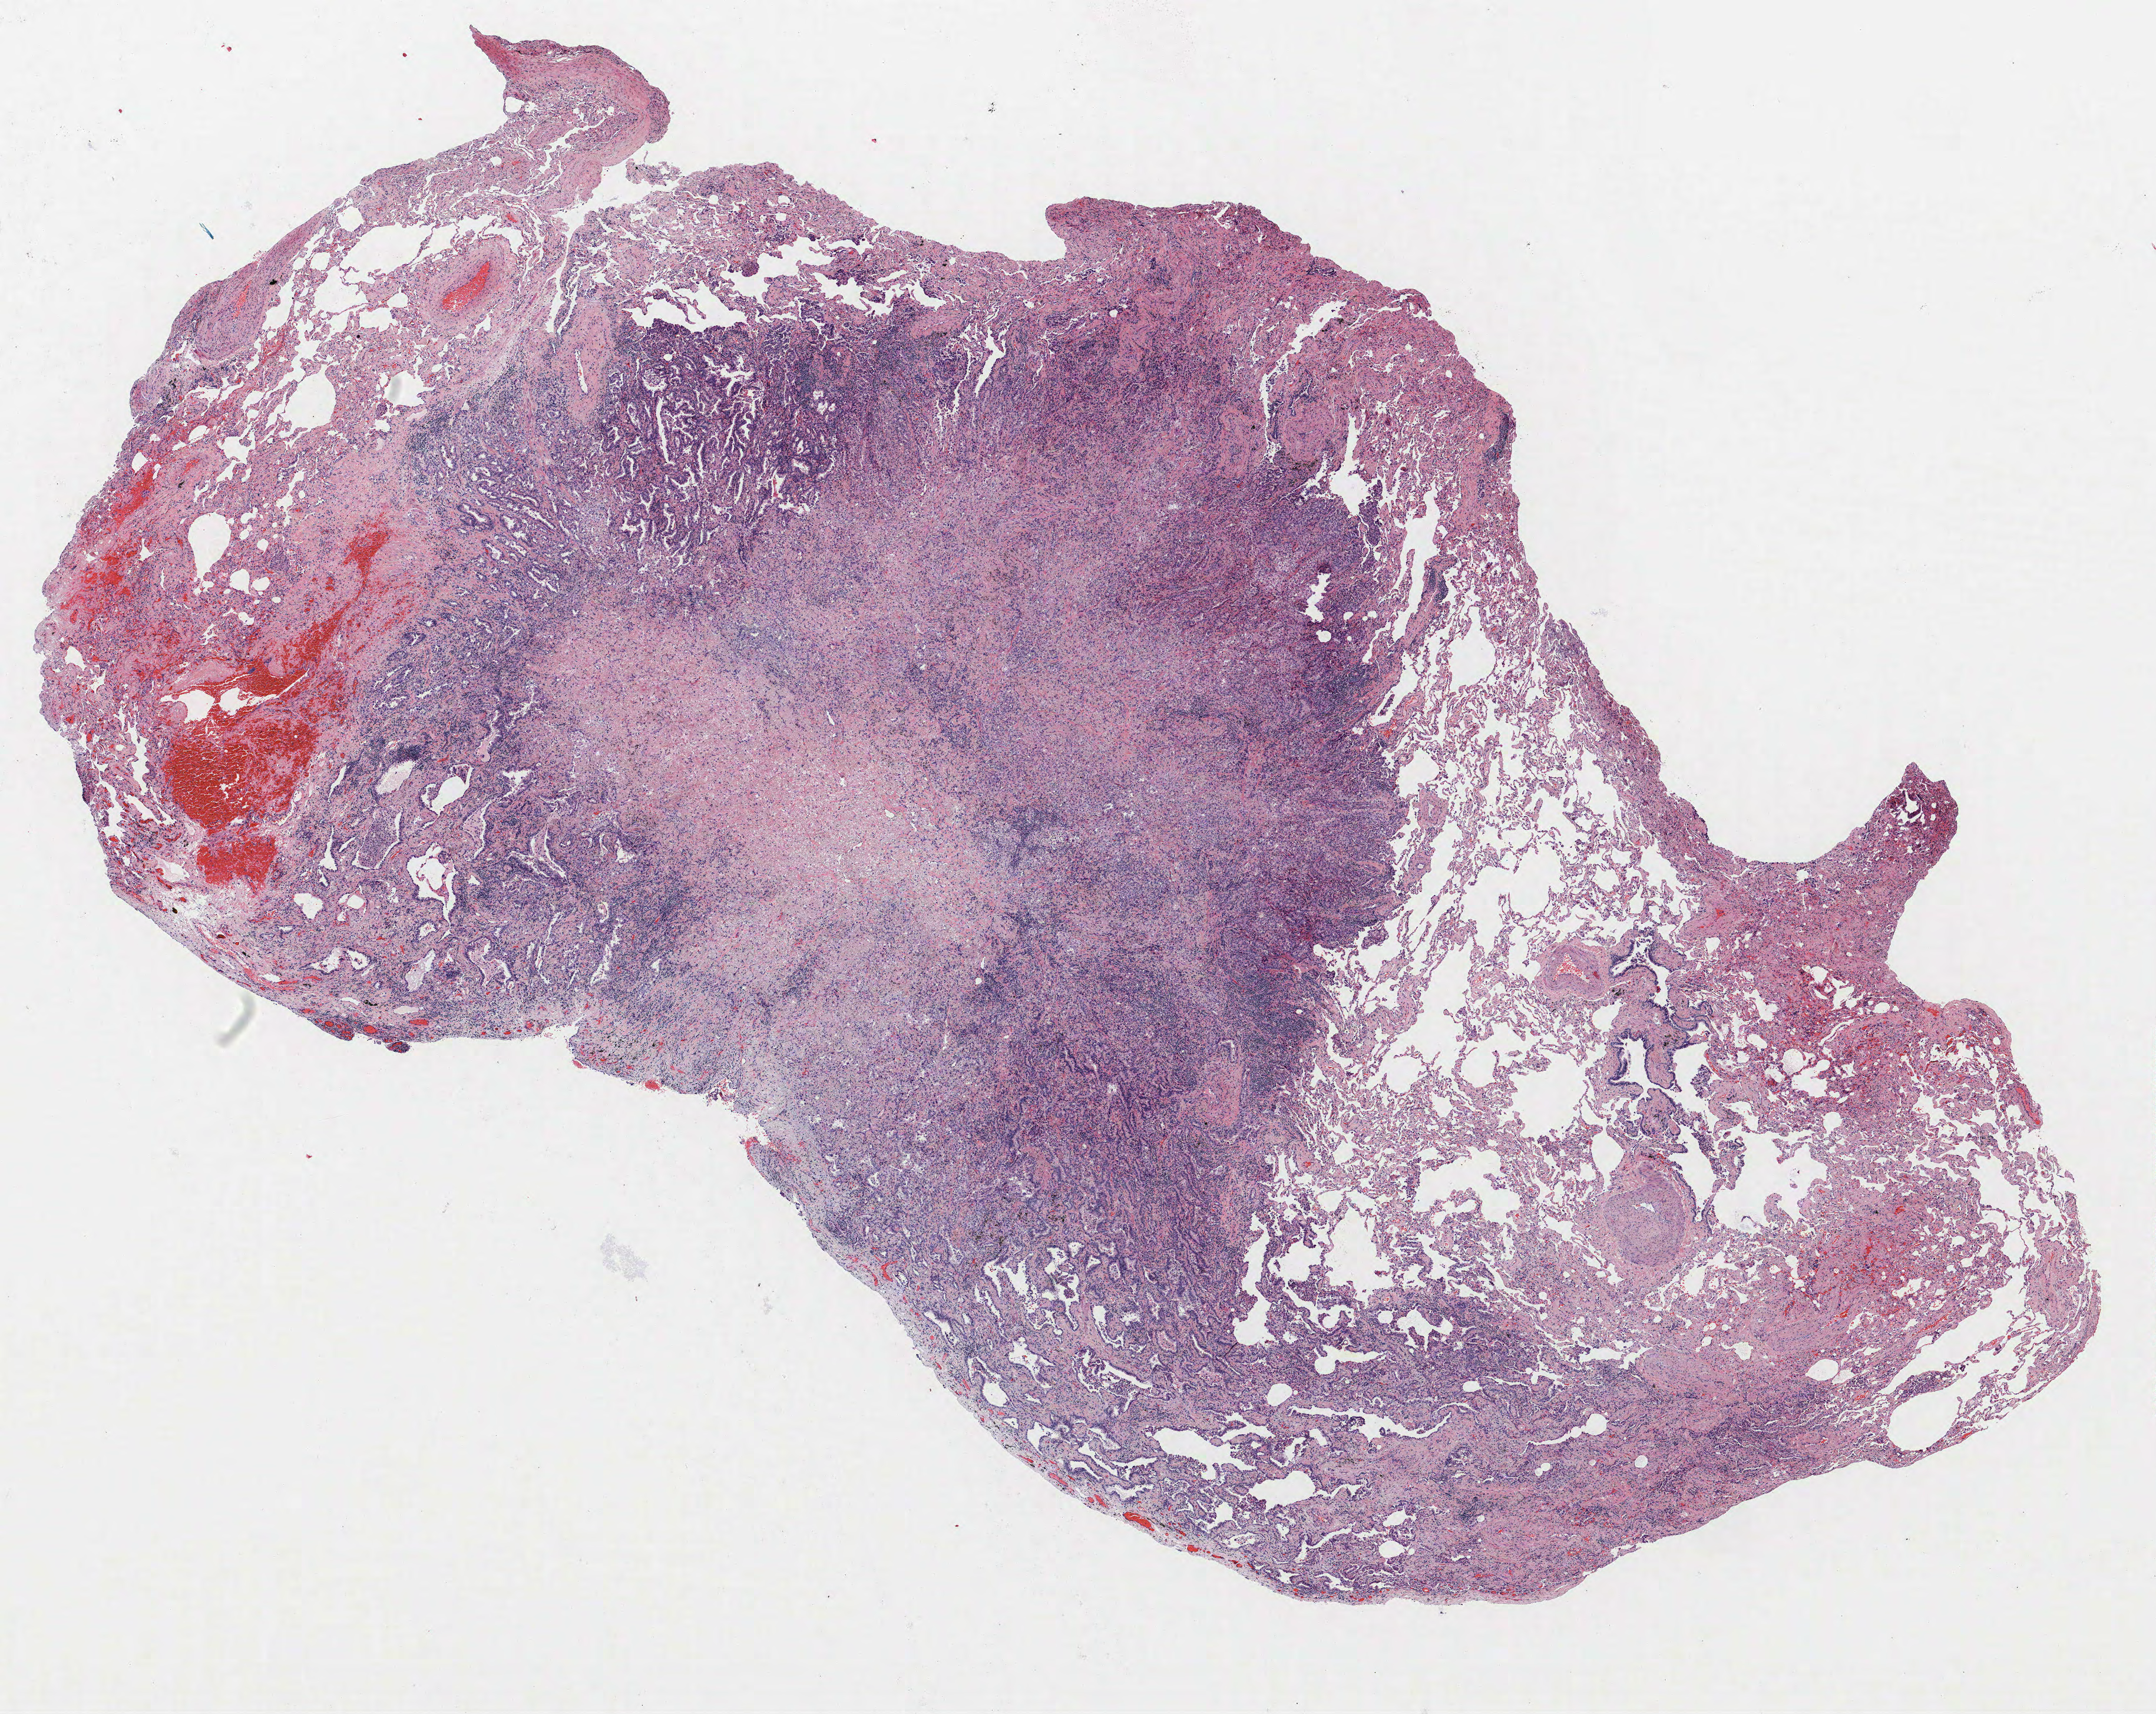
Whole-slide histology image, Hematoxylin and eosin (H&E) stained, whole scanned area (about 14.6 x 11.6 mm) shown as a low-resolution overview; formalin-fixed paraffin-embedded (FFPE) section; lung tissue. Male, age 62 at enrolment. Former smoker at enrolment. Grade: moderately differentiated (G2).
Primary tumour location (clinical record): right upper lobe. Participant's lung-cancer diagnosis: Adenocarcinoma, NOS (ICD-O-3 8140/3). Tumour size (pathology): 7 mm. Stage (AJCC 6th edition): IA.